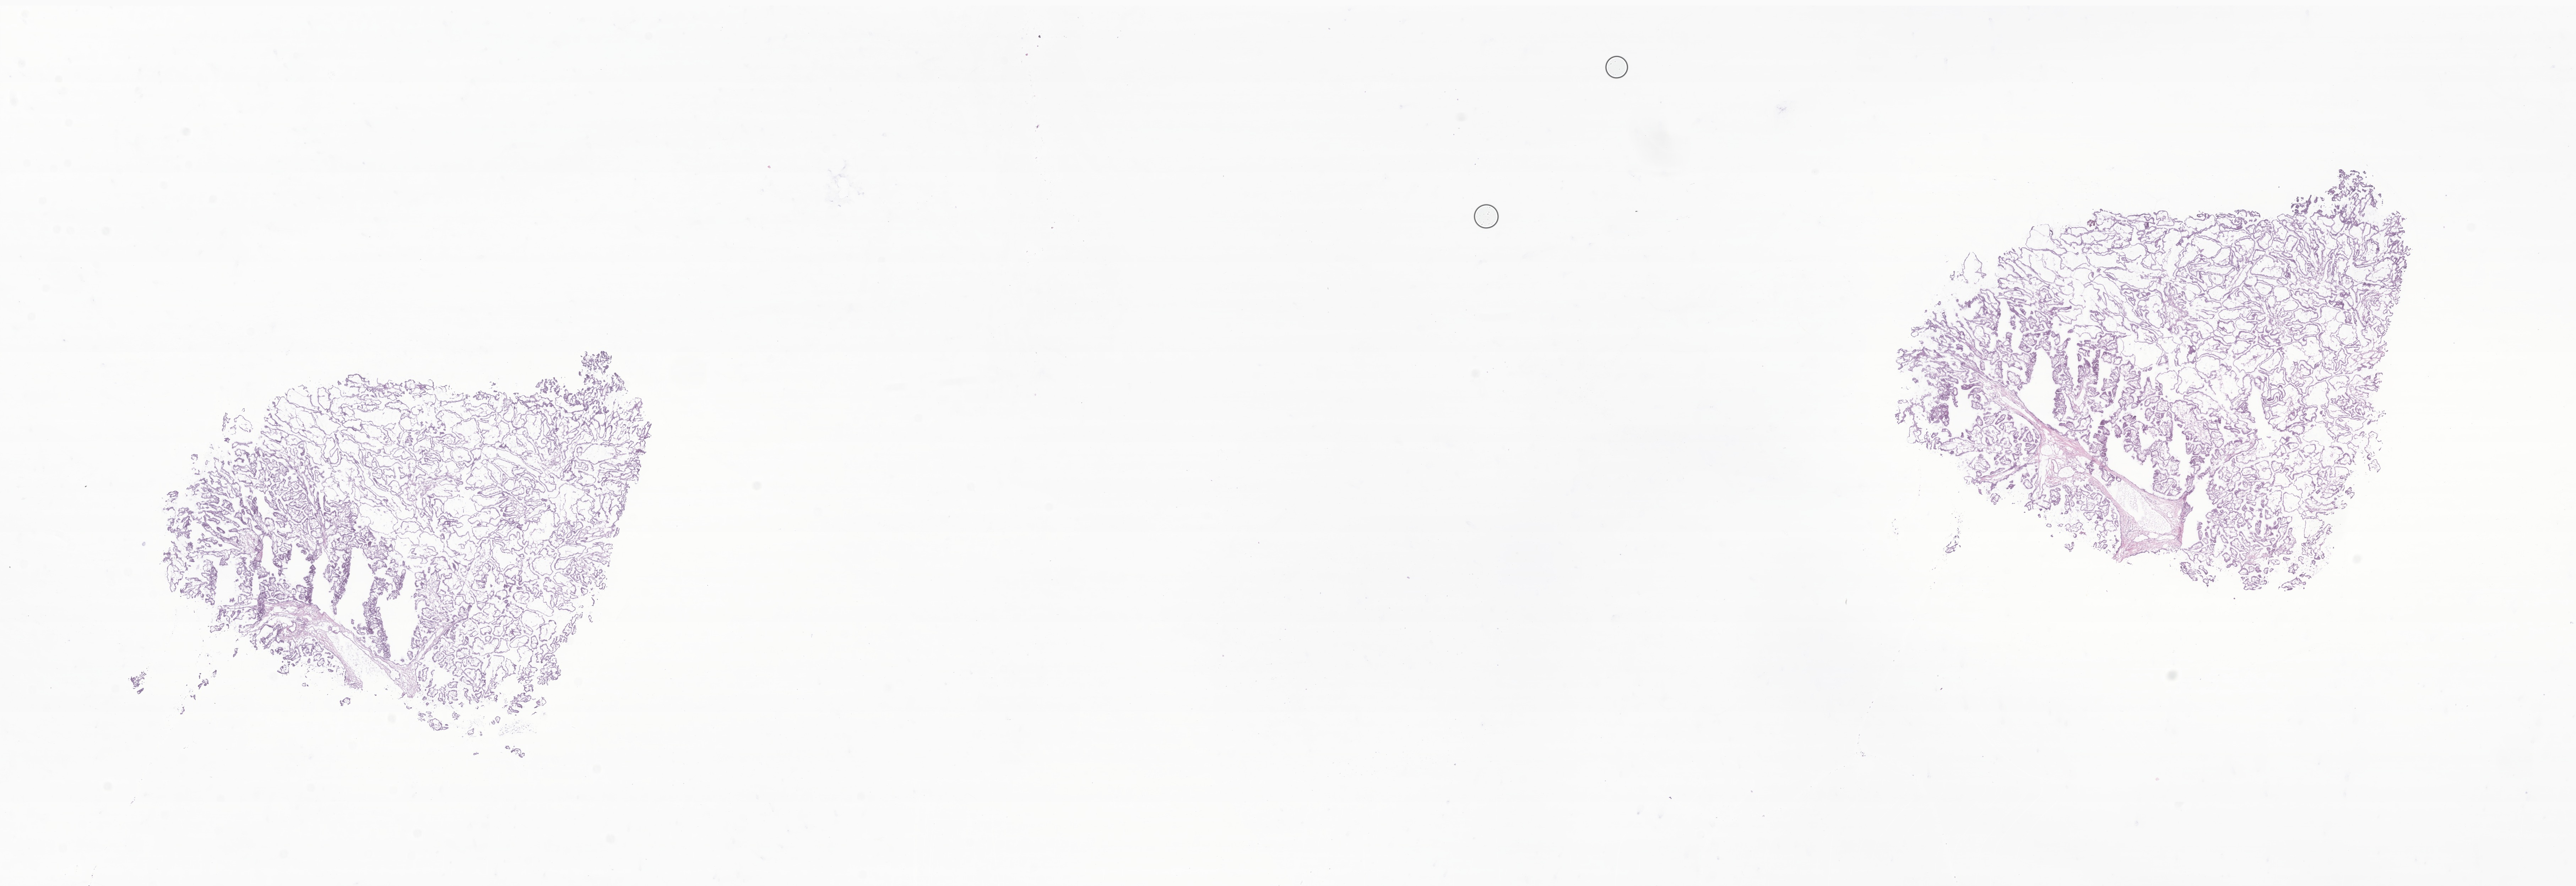
Digitized H&E-stained section of tumor tissue from the brain — low-resolution overview of the scanned area, about 30.6 x 10.5 mm, frozen section. Patient male; age 647 days.
• diagnosis: Neoplasm, uncertain whether benign or malignant